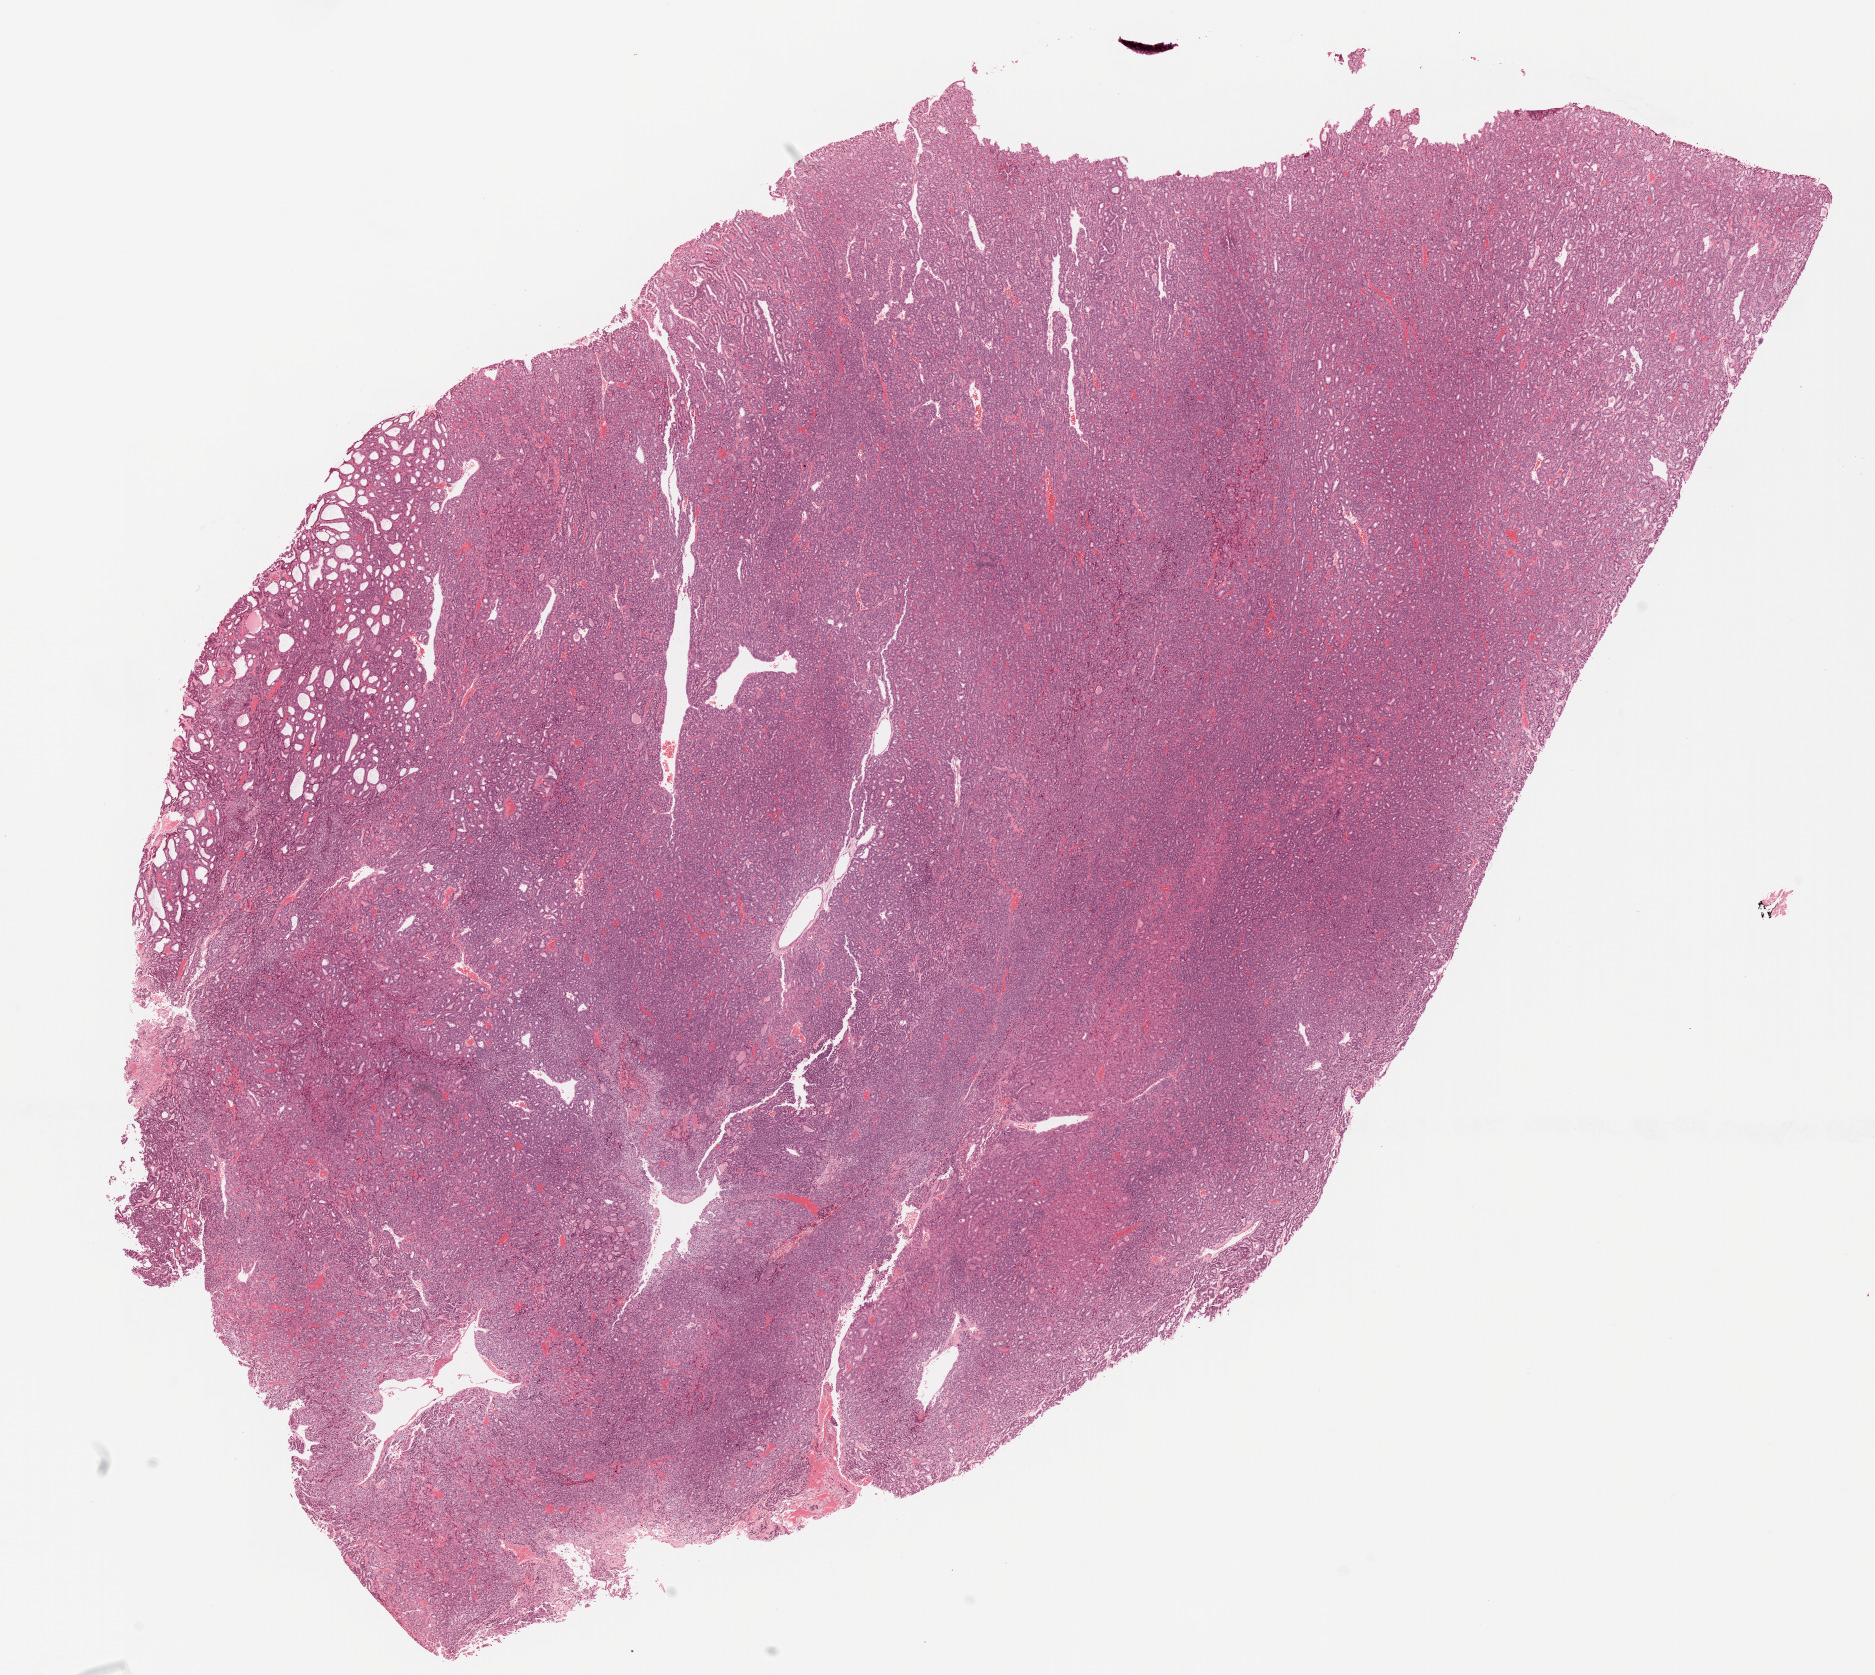
H&E-stained whole-slide image — whole scanned area (about 15.0 x 13.4 mm) shown as a low-resolution overview. FFPE section. Sample: primary tumour, thyroid. Patient: female, age at initial diagnosis 62 years.
Histologic diagnosis: Papillary carcinoma, follicular variant (thyroid gland).